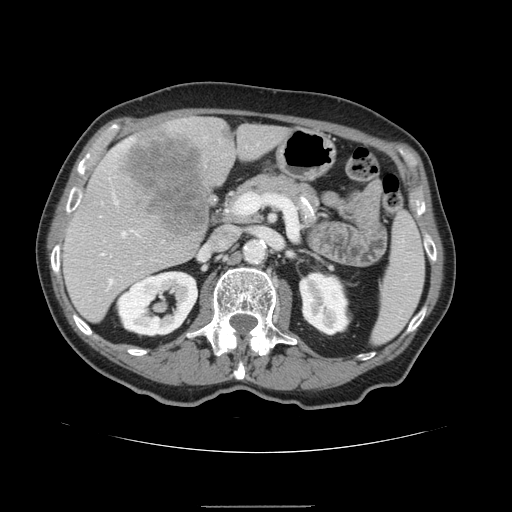
Contrast-enhanced abdominal CT, one axial slice; 120 kVp; intravenous contrast given; soft-tissue window (W 400 / L 40 HU); 2.5 mm slice thickness; 512 × 512 image matrix. Male patient, age 74 years. From the clinical record (not read from this slice): diagnosis: colorectal cancer liver metastases, imaged before liver resection; multiple liver metastases: no; largest metastasis: 14.5 cm; disease in both lobes: yes.
Structures marked on this image (outlined manually by an expert reader):
- hepatic veins: box from (x=110, y=232) to (x=126, y=281) px
- liver: (x=62, y=117)–(x=290, y=323)
- planned liver remnant (the part of the liver to remain after resection): (x=63, y=124)–(x=289, y=324)
- portal vein (with intrahepatic branches): (x=100, y=252)–(x=157, y=261)
- liver metastasis: (x=121, y=125)–(x=214, y=239)